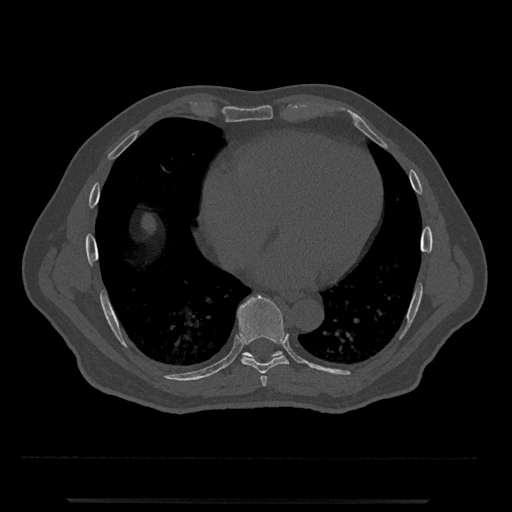
CT including the spine, one axial slice. Slice 616 of 797 in the series (ordered by position). 120 kVp. Bone window (W 1800 / L 400 HU). 0.5 mm slice thickness. 512 × 512 image matrix, field of view 419 × 419 mm. Patient: male, 63 years. Case-level facts recorded for this patient, not image findings: primary cancer: prostate.
Structures marked on this image (semi-automatically segmented with operator editing):
- T7 vertebra: bounding box (x1, y1, x2, y2) in pixels: (260, 375, 268, 387)
- T8 vertebra: (237, 295, 289, 374)
- T9 vertebra: (242, 351, 283, 362)